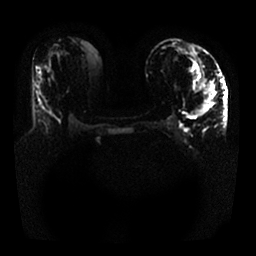
Breast MRI, one axial slice; position 10 of 25 along the scan axis; diffusion-weighted series; image 2 of 4 stored at this slice position (different b-values; order by instance number); 1.5 T; 4 mm slice thickness; 256 × 256 image matrix, field of view 340 × 340 mm. Female patient.
Outlined on this slice (outlined manually by an expert reader):
- tumour on diffusion-weighted imaging: bounding box [x1, y1, x2, y2] px = [195, 79, 216, 115]